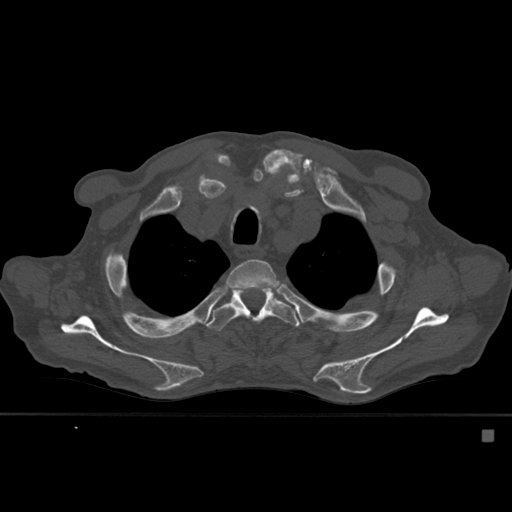
CT including the spine, one axial slice; position 423 of 527 along the scan axis; bone window (W 1800 / L 400 HU); 1.5 mm slice thickness; 512 × 512 image matrix, field of view 373 × 373 mm. Patient: male, 78 years. Case-level facts recorded for this patient, not image findings: primary cancer: prostate.
Outlined on this slice (semi-automatic segmentation, software-assisted and operator-edited):
- T3 vertebra: bounding box [x1, y1, x2, y2] px = [225, 259, 281, 289]
- T4 vertebra: [206, 286, 301, 331]